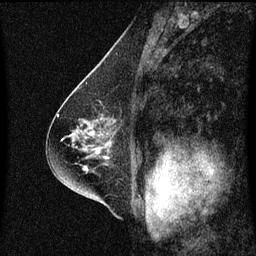
Breast MRI (dynamic contrast-enhanced), one sagittal slice. Slice 38 of 60 in the series (ordered by position). Dynamic contrast-enhanced series, image 2 of 3 at this slice position (ordered by acquisition). 1.5 T. TE 4.2 ms, TR 8.4 ms. 2 mm slice thickness. 256 × 256 image matrix, field of view 200 × 200 mm. Female patient, age 58 years.
Structures marked on this image (semi-automatic segmentation, software-assisted and operator-edited):
- analysis volume of interest (the breast-tissue region the enhancement analysis was run in; not a lesion): bounding box [x1, y1, x2, y2] px = [86, 102, 122, 143]
- tumour enhancement mask (voxels above the 70 % enhancement threshold inside the analysis volume of interest): [113, 120, 115, 123]